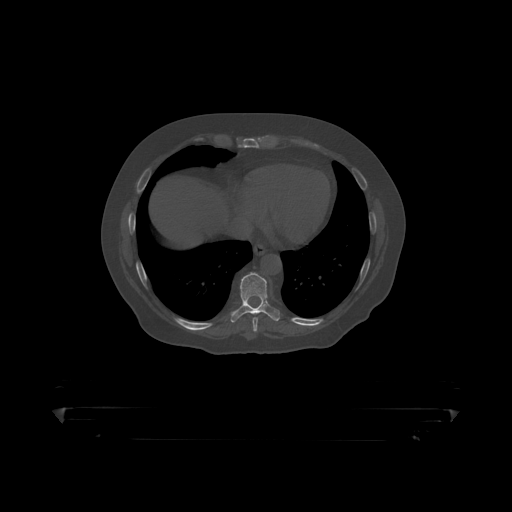
CT including the spine, one axial slice. Slice 240 of 390 in the series (ordered by position). Reconstruction kernel STANDARD. Bone window (W 1800 / L 400 HU). 1.25 mm slice thickness. 512 × 512 image matrix, field of view 650 × 650 mm. Patient: male, 60 years. Case-level facts recorded for this patient, not image findings: primary cancer: prostate.
Structures marked on this image (semi-automatic segmentation, software-assisted and operator-edited):
- T8 vertebra: bounding box <253,317,259,319> (left, top, right, bottom; pixels)
- T9 vertebra: <231,273,281,318>